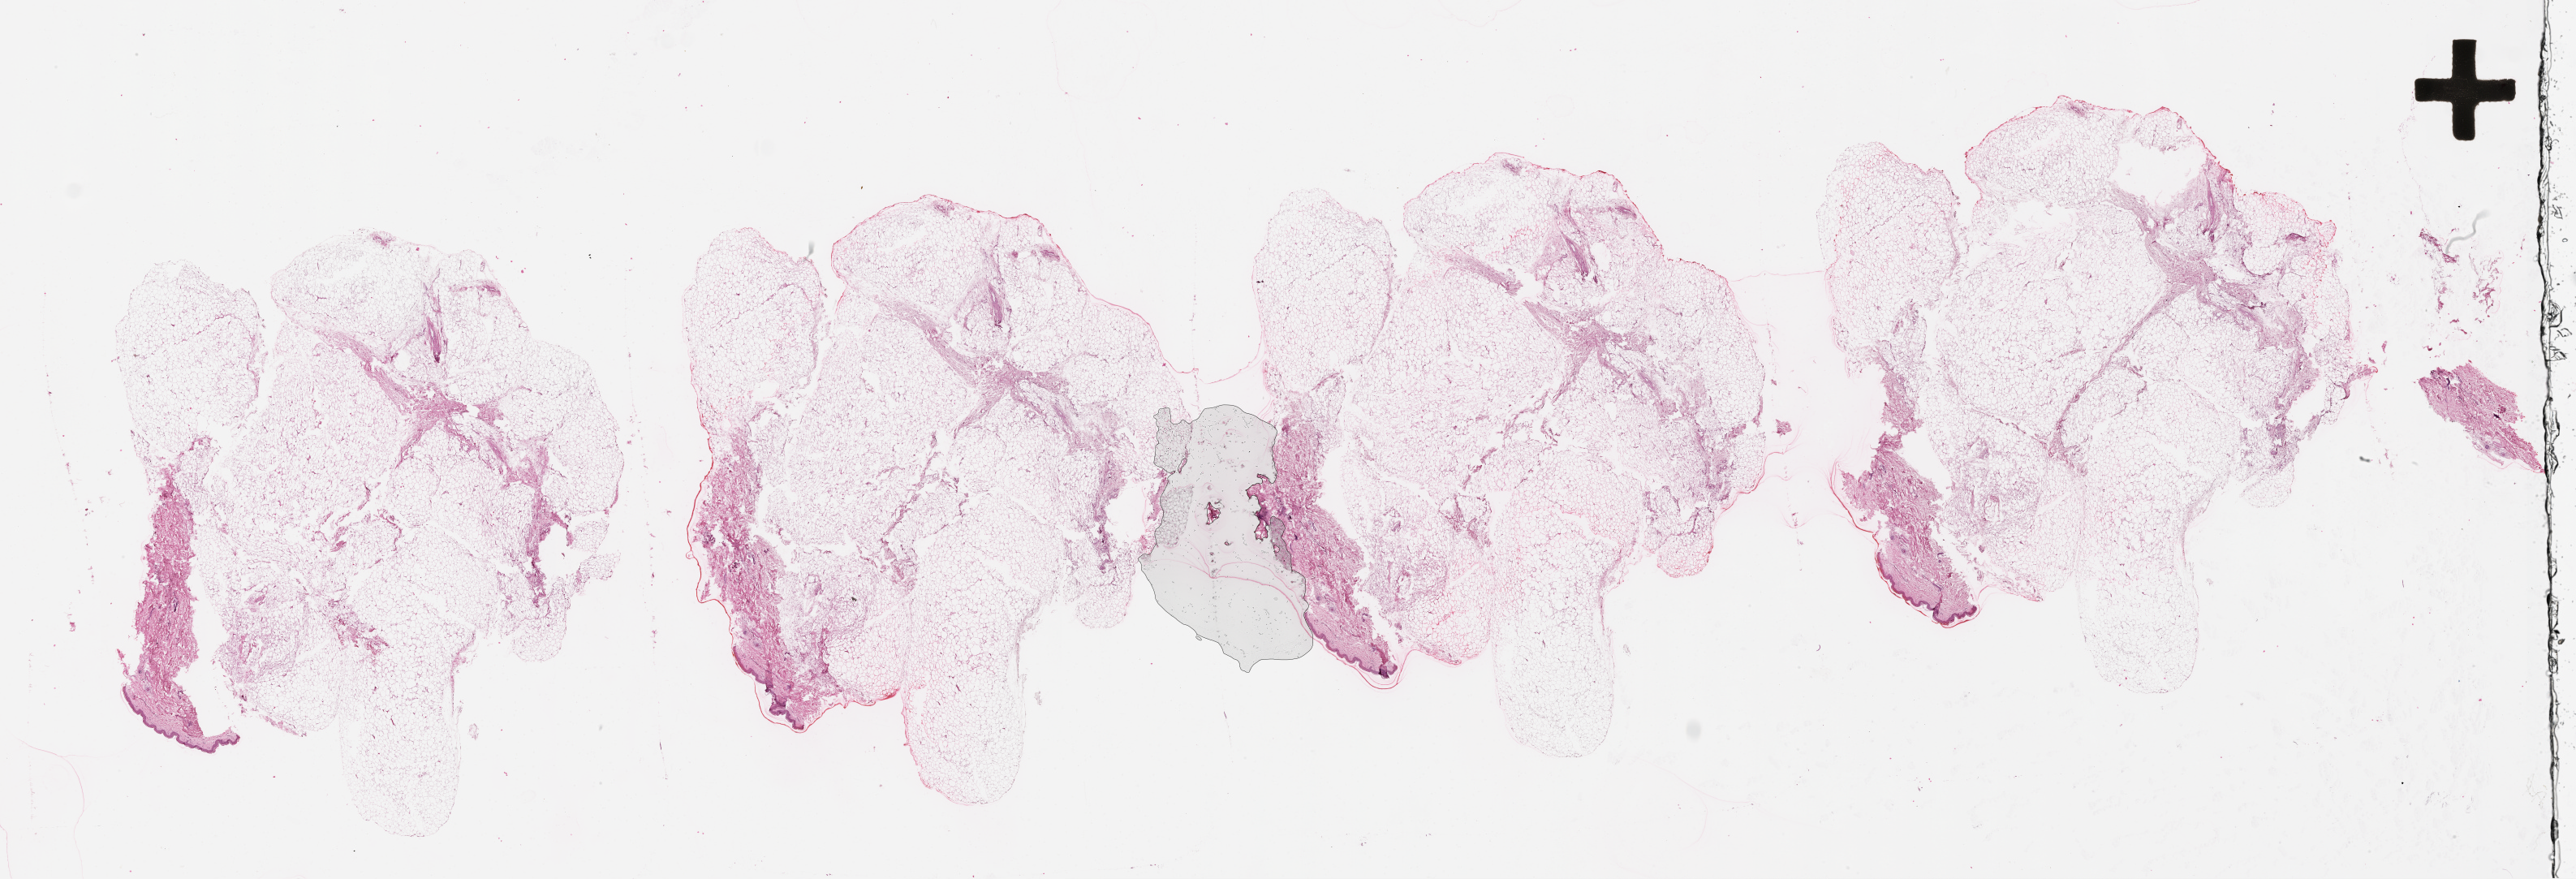
Hematoxylin and eosin (H&E) stained whole-slide image, shown as a low-resolution overview of the whole scanned area (about 51.1 x 17.4 mm). Normal (non-tumour) tissue sample, sampled site: skin. Patient: female, age 76 years.
This section: normal (non-tumour) tissue from the same patient. Patient diagnosis: Malignant melanoma, NOS.